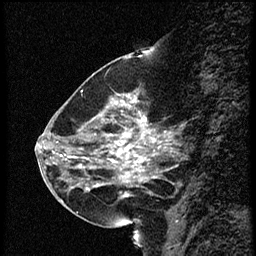
Breast MRI (dynamic contrast-enhanced), one sagittal slice; position 21 of 56 along the scan axis; dynamic contrast-enhanced study with each time point stored as its own series, time point 2 of 4 at this slice position (early post-contrast, ordered by acquisition time); 1.5 T; TE 4.2 ms, TR 18.9 ms; 2 mm slice thickness; 256 × 256 image matrix, field of view 200 × 200 mm. Female patient. Case-level facts recorded for this patient, not image findings: setting: breast cancer imaged before/during neoadjuvant chemotherapy; receptor status: HER2-positive.
Structures marked on this image (semi-automatically segmented with operator editing):
- analysis volume of interest (the breast-tissue region the enhancement analysis was run in; not a lesion): bounding box <63,80,169,215> (left, top, right, bottom; pixels)
- tumour enhancement mask (voxels above the 100 % enhancement threshold inside the analysis volume of interest): <87,94,157,197>